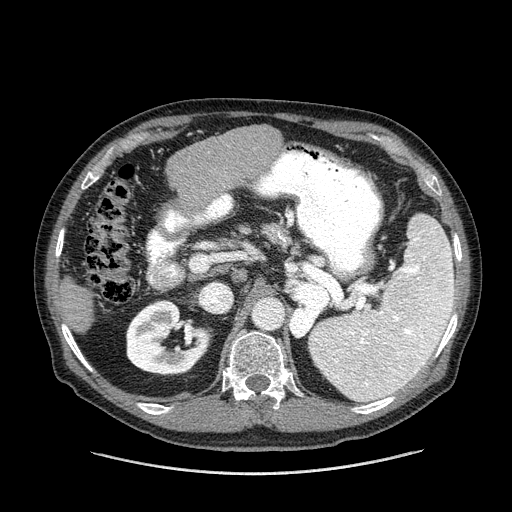
Contrast-enhanced abdominal CT (liver protocol), one axial slice. Position 70 of 180 along the scan axis. 120 kVp. One of 2 acquisitions stored at this slice position. Soft-tissue window (W 400 / L 40 HU). 2.5 mm slice thickness. 512 × 512 image matrix, field of view 420 × 420 mm. From the clinical record (not read from this slice): diagnosis: hepatocellular carcinoma (patient treated with transarterial chemoembolisation; whether this scan precedes or follows treatment is not stated here); TNM stage (as recorded): Stage-II; Child-Pugh class: A; tumour differentiation: well differentiated; tumour size: 2.8 cm.
Outlined on this slice (semi-automatic segmentation, software-assisted and operator-edited):
- liver parenchyma outside the tumour (the mass and vessels are separate outlines, so this box may not span the whole liver): bounding box [x1, y1, x2, y2] px = [57, 126, 282, 332]